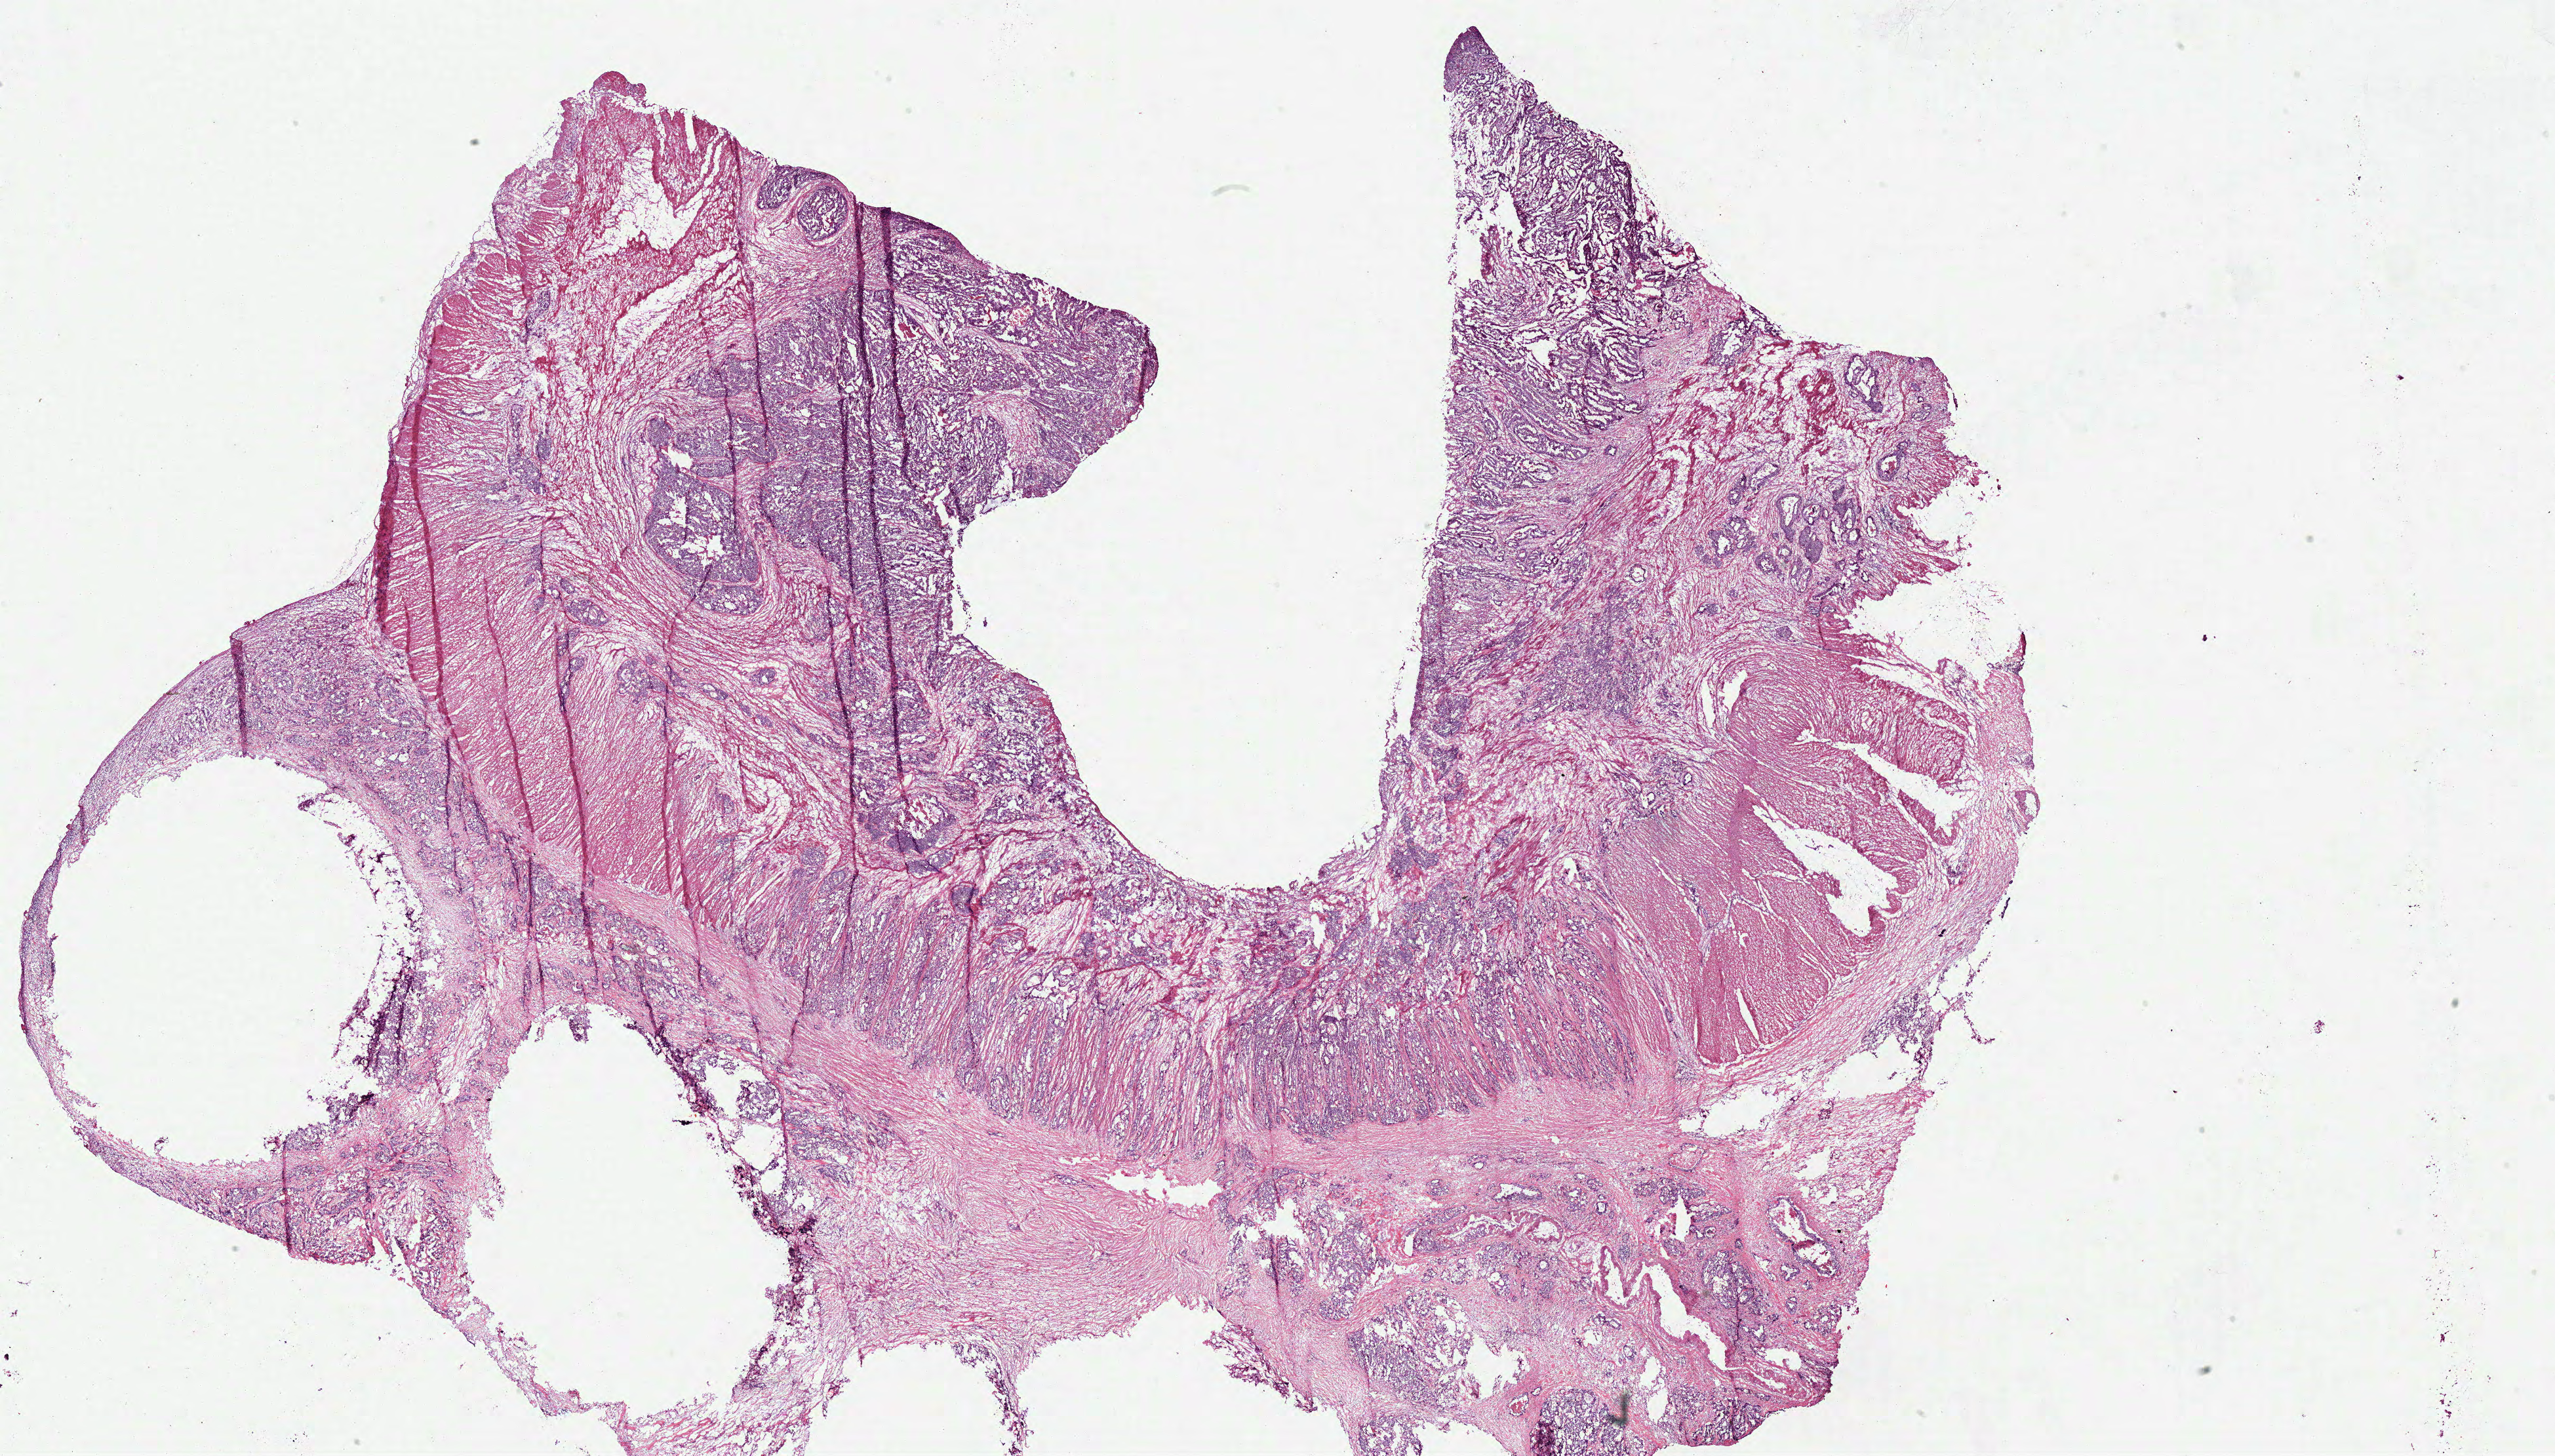
Digitized Hematoxylin and eosin (H&E) stained tissue section (whole slide), shown as a low-resolution overview of the whole scanned area (about 30.7 x 17.5 mm). Frozen section from the bottom of the tissue portion. Primary tumour sample from the colon. Female, age 61 years at initial diagnosis. Pathologist review of this section (percent, as recorded): tumour cells 80%, tumour nuclei 80%, normal cells 0%, stromal cells 20%, necrosis 0%. Inflammatory infiltration, as recorded: lymphocyte infiltration 5%, monocyte infiltration 0%, neutrophil infiltration 0%.
• lymph nodes positive (case pathology): 6 of 6 examined
• pathologic diagnosis: Adenocarcinoma, NOS
• AJCC pathologic stage: IIIB (7th edition)
• TNM: T3 N2a M0